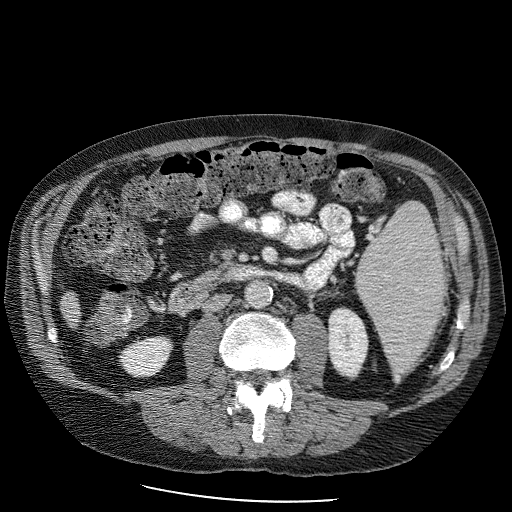
Contrast-enhanced abdominal CT (liver protocol), one axial slice; slice 21 of 98 in the series (ordered by position); reconstruction kernel STANDARD; soft-tissue window (W 400 / L 40 HU); 512 × 512 image matrix. Case-level facts recorded for this patient, not image findings: diagnosis: hepatocellular carcinoma (patient treated with transarterial chemoembolisation; whether this scan precedes or follows treatment is not stated here); TNM stage (as recorded): Stage-II; Child-Pugh class: B; tumour differentiation: moderately differentiated; tumour nodularity: uninodular.
Outlined on this slice (semi-automatically segmented with operator editing):
- liver parenchyma outside the tumour (the mass and vessels are separate outlines, so this box may not span the whole liver): bounding box [x1, y1, x2, y2] px = [58, 277, 82, 328]